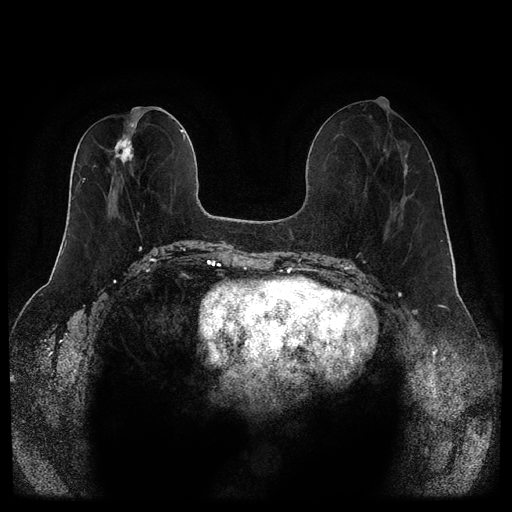
Breast MRI (dynamic contrast-enhanced, multi-phase), one axial slice. Position 43 of 116 along the scan axis. Dynamic contrast-enhanced series, time point 2 of 5 at this slice position (early post-contrast). 1.5 T. TE 2.6 ms, TR 5.3 ms. 2 mm slice thickness. 512 × 512 image matrix, field of view 350 × 350 mm. Female patient, age 46 years.
Outlined on this slice (semi-automatically segmented with operator editing):
- breast lesion (labelled 'tumour' in the annotation; benign lesions carry a separate 'benign' label): bounding box [x1, y1, x2, y2] px = [113, 130, 135, 166]